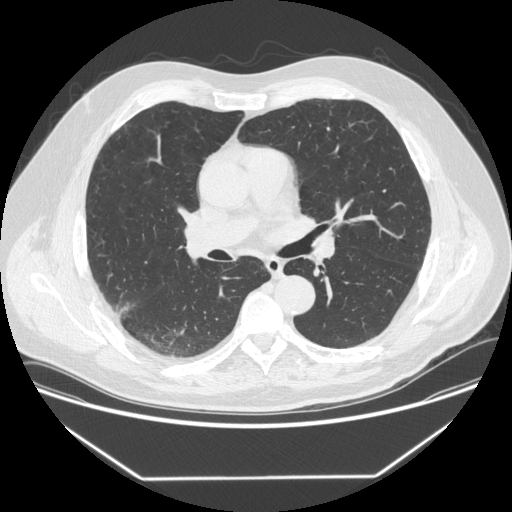
Low-dose screening chest CT, one axial slice. Position 206 of 342 along the scan axis. Reconstruction kernel STANDARD. 120 kVp. Lung window (W 1500 / L -600 HU). 1.25 mm slice thickness. 512 × 512 image matrix.
Annotated regions visible in this slice (expert manual segmentation):
- lesion 1 (tumor, upper lobe of right lung): bounding box [x1, y1, x2, y2] px = [118, 304, 129, 317]